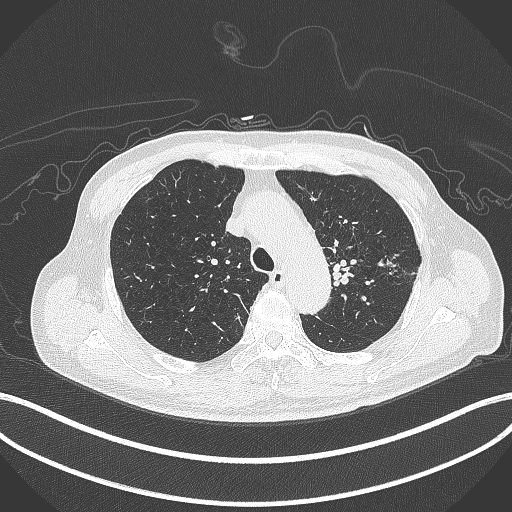
Chest CT, one axial slice; slice 327 of 417 in the series (ordered by position); 120 kVp; lung window (W 1500 / L -600 HU); 1 mm slice thickness; 512 × 512 image matrix. Male patient, age 77 years. Case-level facts recorded for this patient, not image findings: clinical TNM (as recorded): T3 N1 M0.
Outlined on this slice (bounding box drawn by a radiologist):
- lung tumour (recorded histology: adenocarcinoma): bounding box [x1, y1, x2, y2] px = [374, 253, 398, 270]